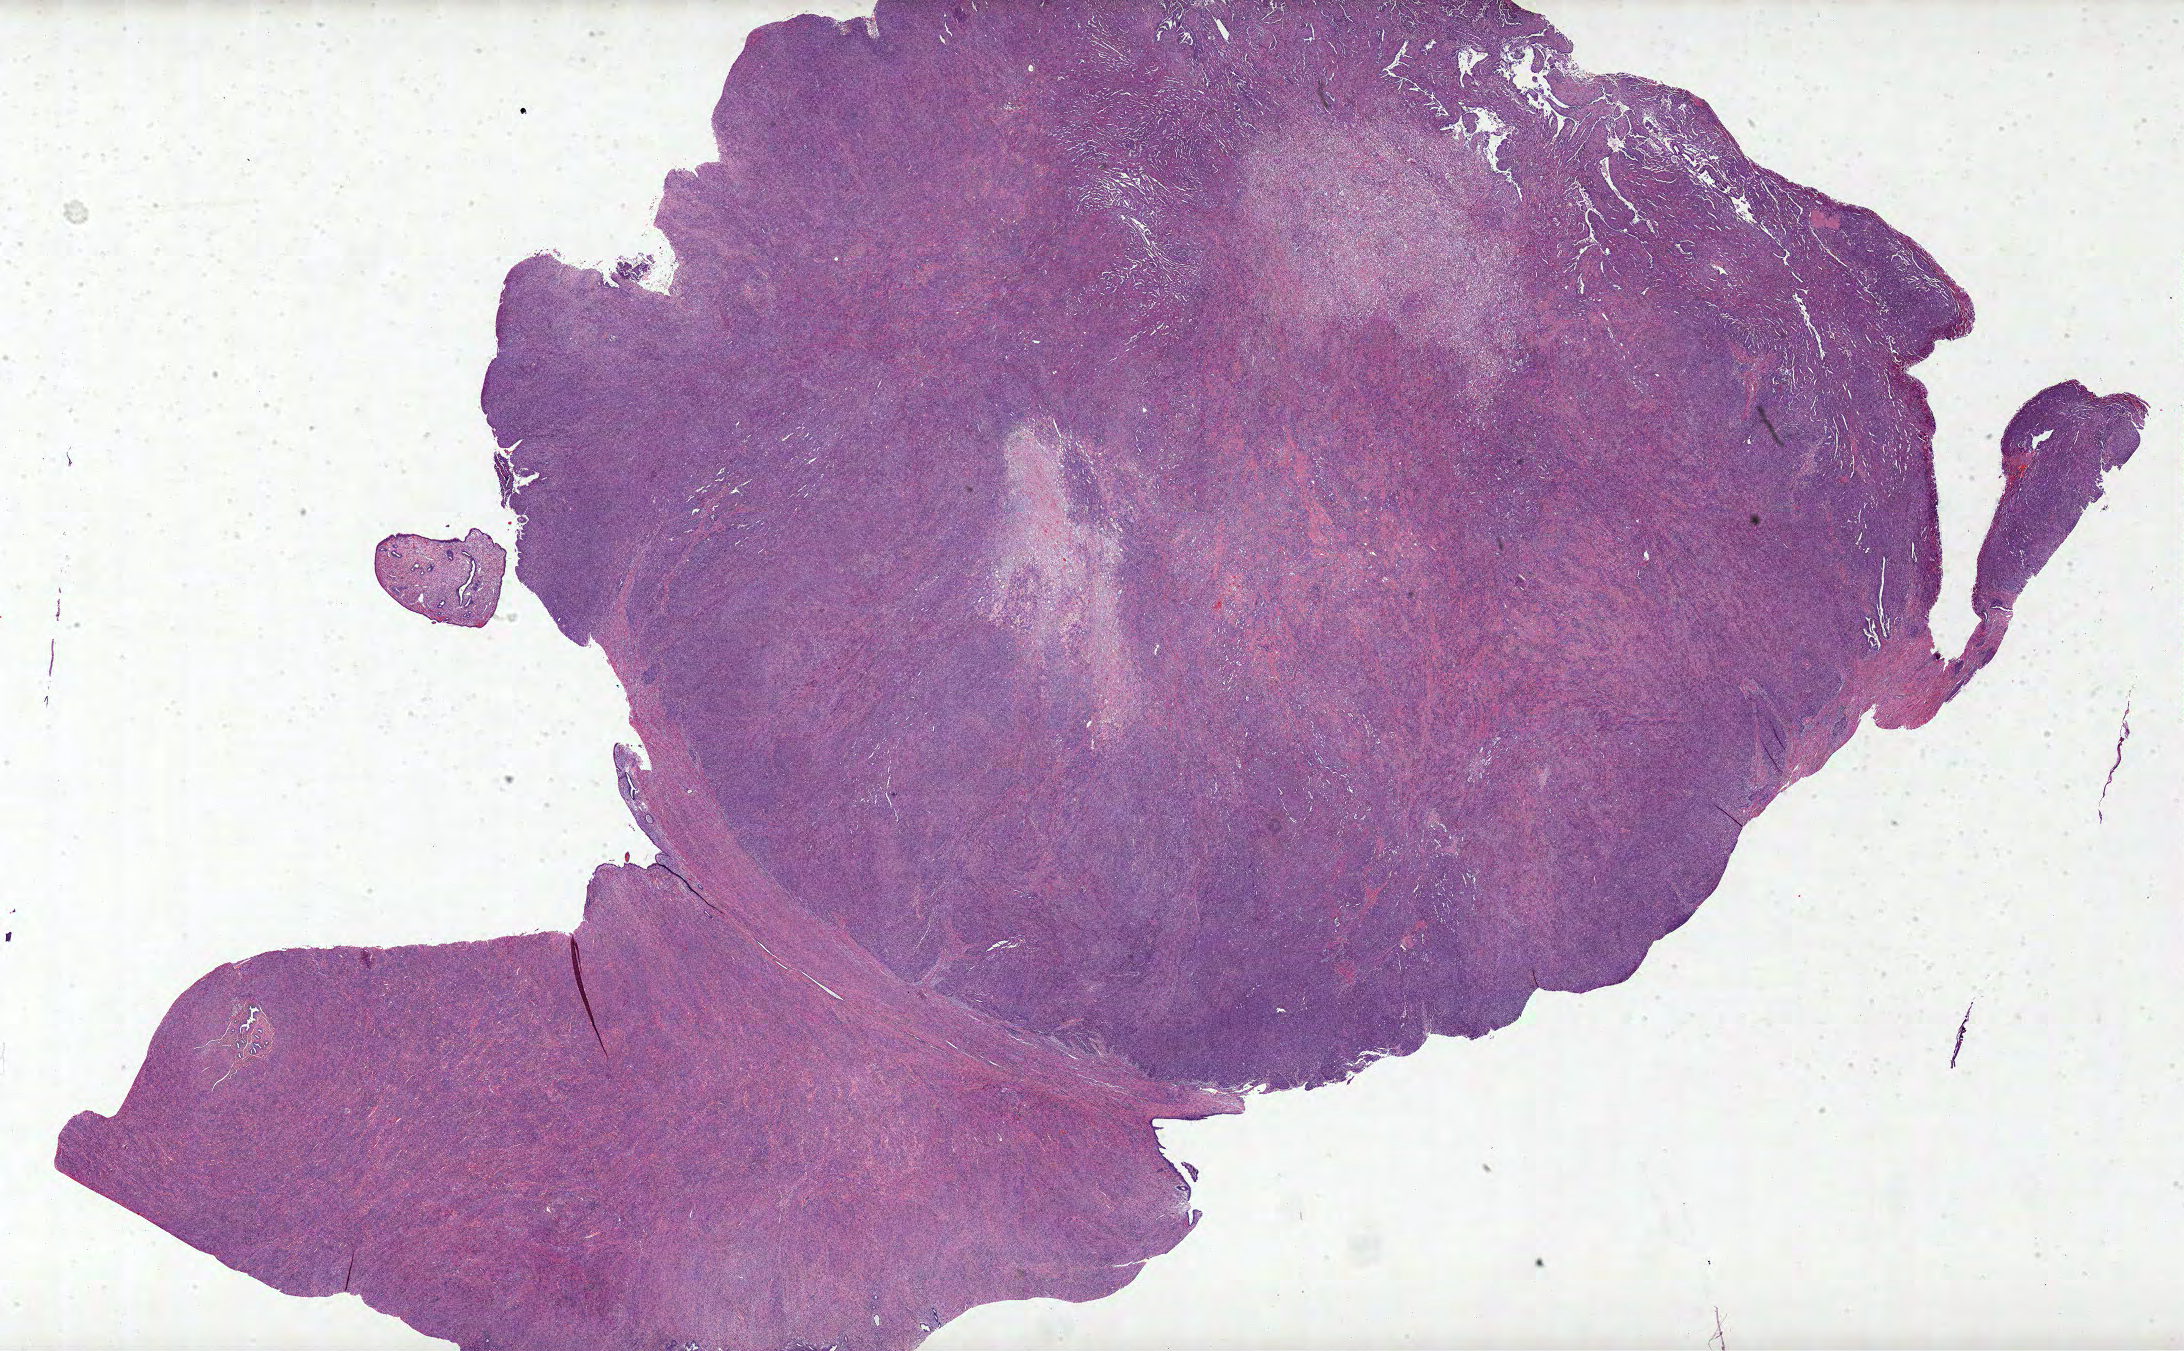
Hematoxylin and eosin (H&E) stained whole-slide image — shown as a low-resolution overview of the whole scanned area (about 34.8 x 21.5 mm). Formalin-fixed paraffin-embedded (FFPE) diagnostic section. Uterus, primary tumour sample. Female, age 75 years at initial diagnosis. Histologic grade: G3 (poorly differentiated).
- FIGO stage: IB
- histologic diagnosis: Serous cystadenocarcinoma, NOS (endometrium)